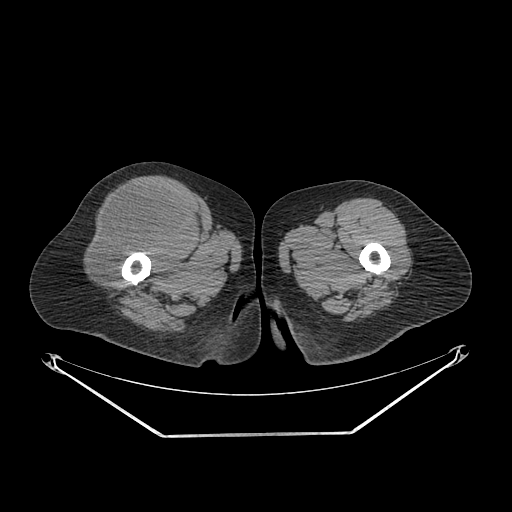
CT of an extremity soft-tissue mass (from a PET/CT study), one axial slice. Slice 263 of 311 in the series (ordered by position). Reconstruction kernel SOFT. 140 kVp. Soft-tissue window (W 400 / L 40 HU). 3.75 mm slice thickness. 512 × 512 image matrix. Female patient. From the clinical record (not read from this slice): histological type: pleiomorphic undifferentiated sarcoma; grade: high; site of the primary tumour: right quadricep.
Structures marked on this image (expert contour drawn on MRI and transferred to this co-registered scan by the dataset authors):
- tumour plus oedema (research contour): box from (x=91, y=187) to (x=191, y=282) px
- tumour (research contour): (x=91, y=187)–(x=191, y=282)